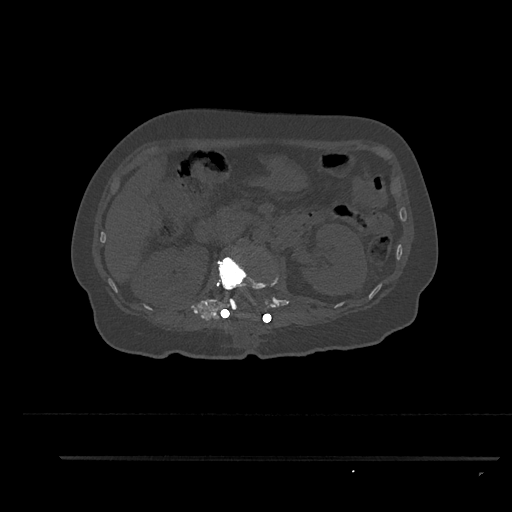
CT including the spine, one axial slice; position 199 of 797 along the scan axis; 120 kVp; bone window (W 1800 / L 400 HU); 512 × 512 image matrix, field of view 408 × 408 mm. Patient: female, 44 years. From the clinical record (not read from this slice): primary cancer: renal; vertebrae with lytic lesions (as recorded): L1.
Outlined on this slice (semi-automatically segmented with operator editing):
- L1 vertebra: bounding box [x1, y1, x2, y2] px = [218, 246, 278, 318]